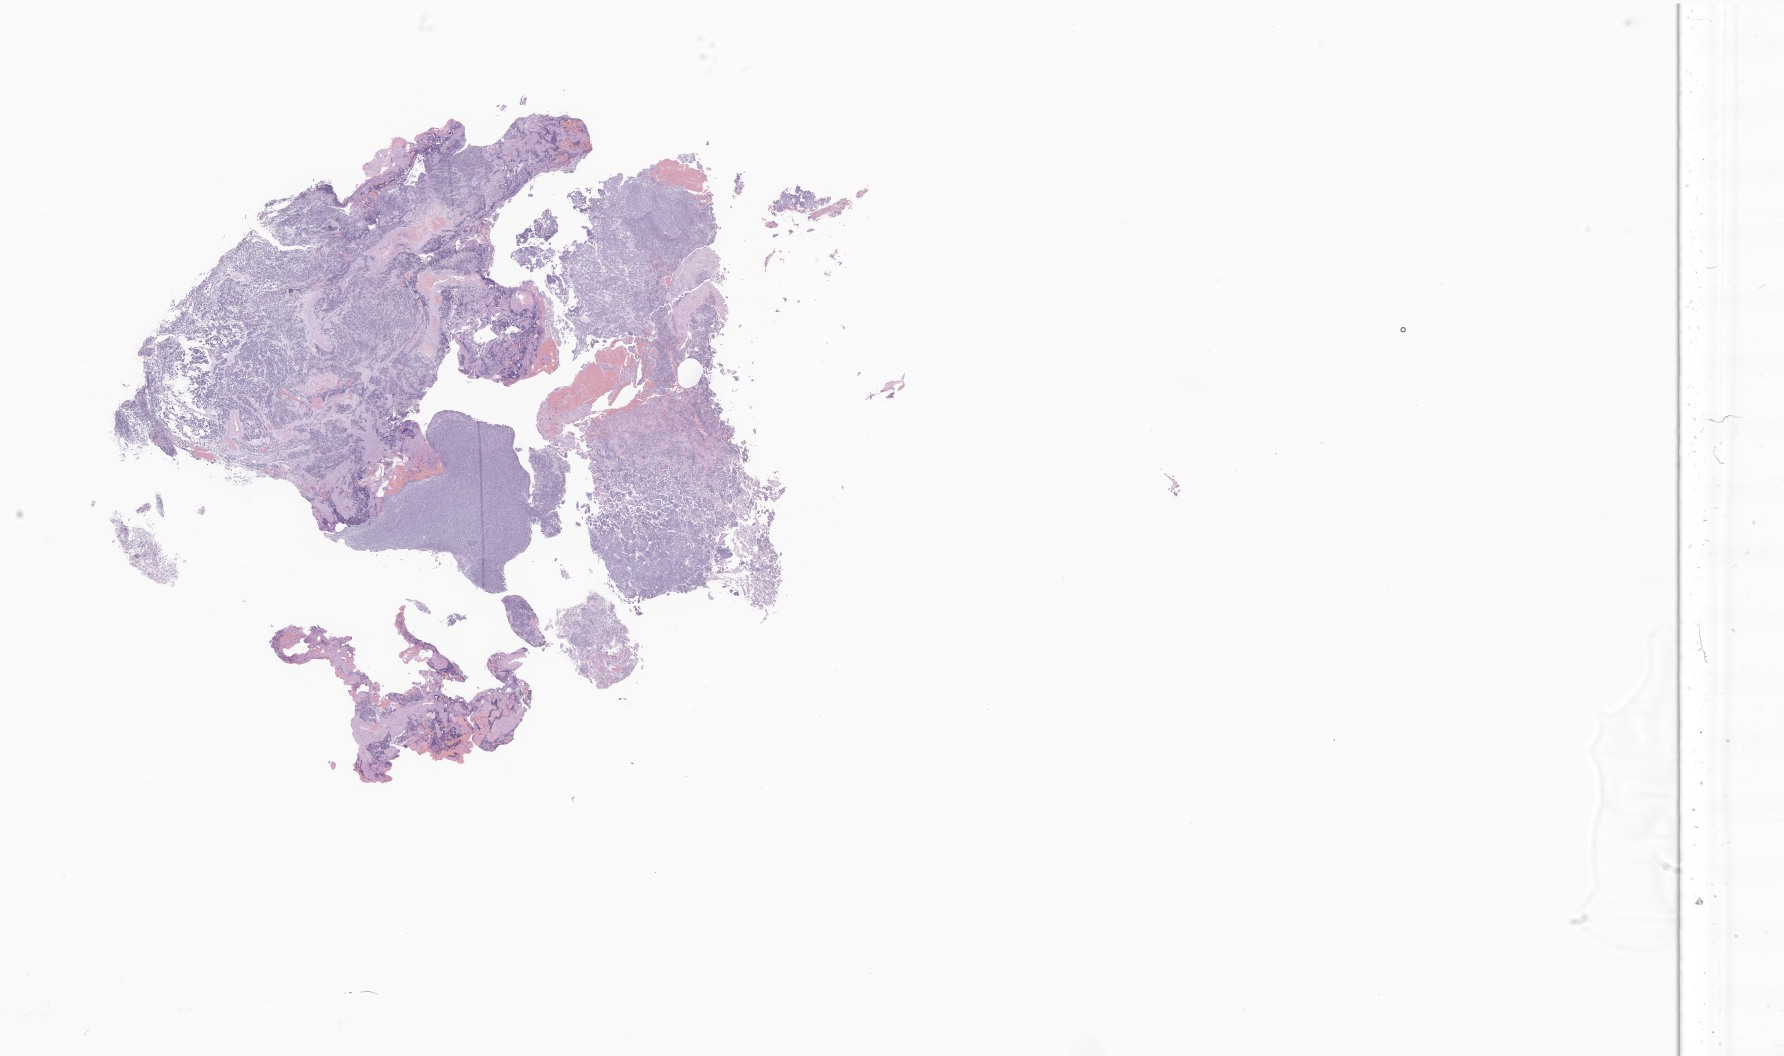
Digitized haematoxylin and eosin-stained section of tumor tissue from the cerebellum — low-resolution overview of the scanned area, about 30.1 x 17.8 mm. Formalin-fixed, paraffin-embedded (FFPE) tissue. Patient: male, age 903 days (about 2.5 years).
Diagnosis (ICD-O-3 morphology term): Medulloblastoma, NOS.